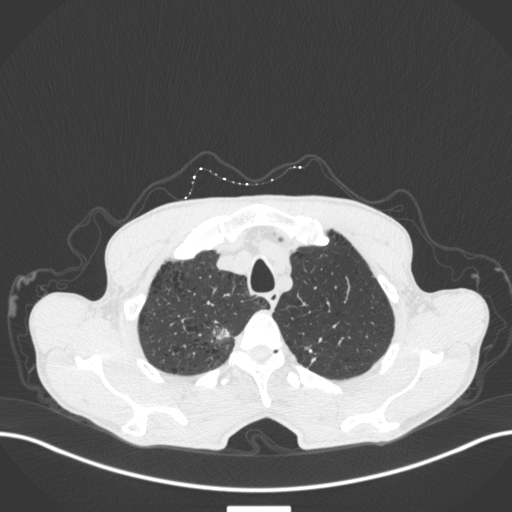
Chest CT, one axial slice; position 368 of 445 along the scan axis; reconstruction kernel B31f; 120 kVp; lung window (W 1500 / L -600 HU); 1 mm slice thickness; 512 × 512 image matrix, field of view 400 × 400 mm. Male patient, age 70 years. Case-level facts recorded for this patient, not image findings: clinical TNM (as recorded): T1a N0 M0; histopathological grade: G1-2.
Annotated regions visible in this slice (bounding box drawn by a radiologist):
- lung tumour (recorded histology: adenocarcinoma): bounding box <205,315,232,341> (left, top, right, bottom; pixels)